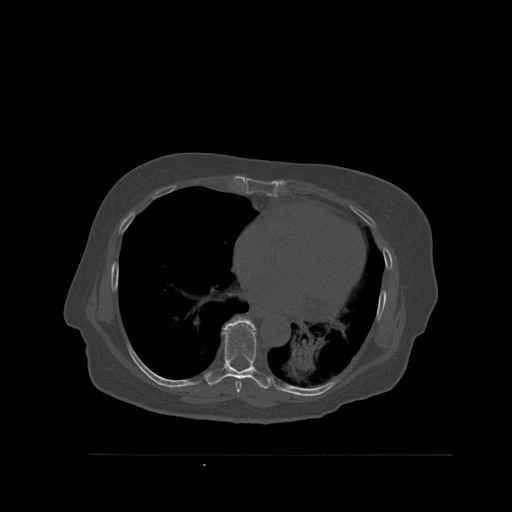
CT including the spine, one axial slice; slice 352 of 527 in the series (ordered by position); bone window (W 1800 / L 400 HU); 1.5 mm slice thickness; 512 × 512 image matrix. Female patient, age 73 years. Case-level facts recorded for this patient, not image findings: primary cancer: breast; vertebrae with lytic lesions (as recorded): L2.
Outlined on this slice (semi-automatically segmented with operator editing):
- T7 vertebra: bounding box <235,379,242,393> (left, top, right, bottom; pixels)
- T8 vertebra: <205,316,272,389>